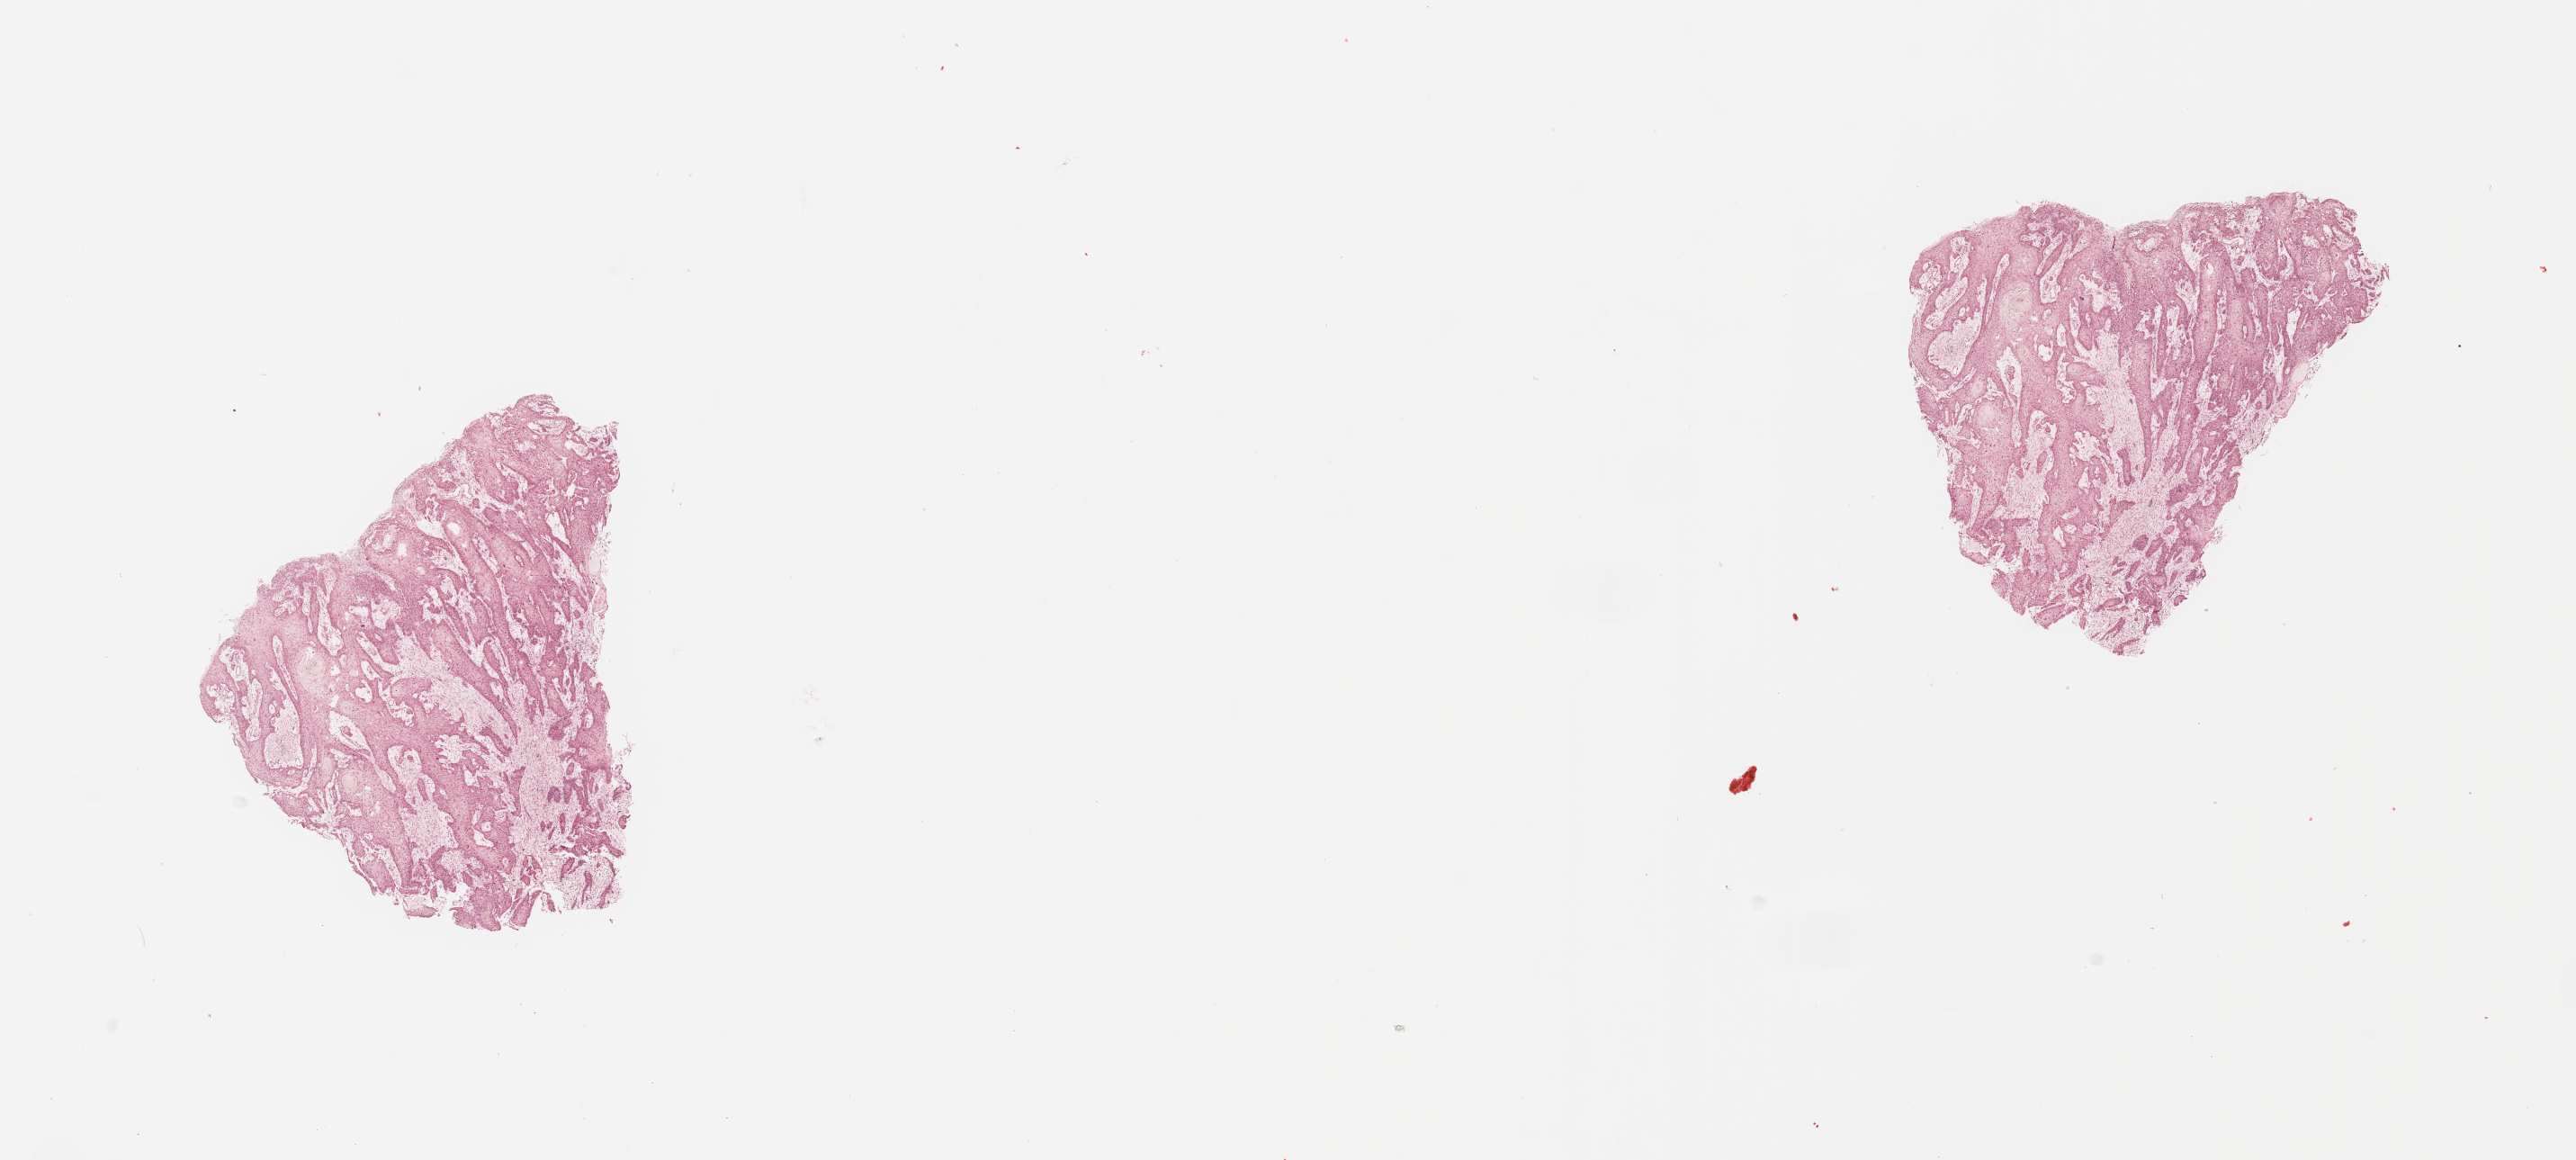
Digitized H&E tissue section (whole slide) — shown as a low-resolution overview of the whole scanned area (about 22.6 x 10.2 mm). Tumour tissue sample, sampled site: tongue. Male, 73 y/o. Histologic grade: G2 (moderately differentiated). Slide review estimates, as recorded: tumour nuclei 80%, necrosis 0%.
AJCC pathologic stage: IVA. Diagnosis: Squamous cell carcinoma, NOS. Primary tumour site (as recorded): oral cavity.